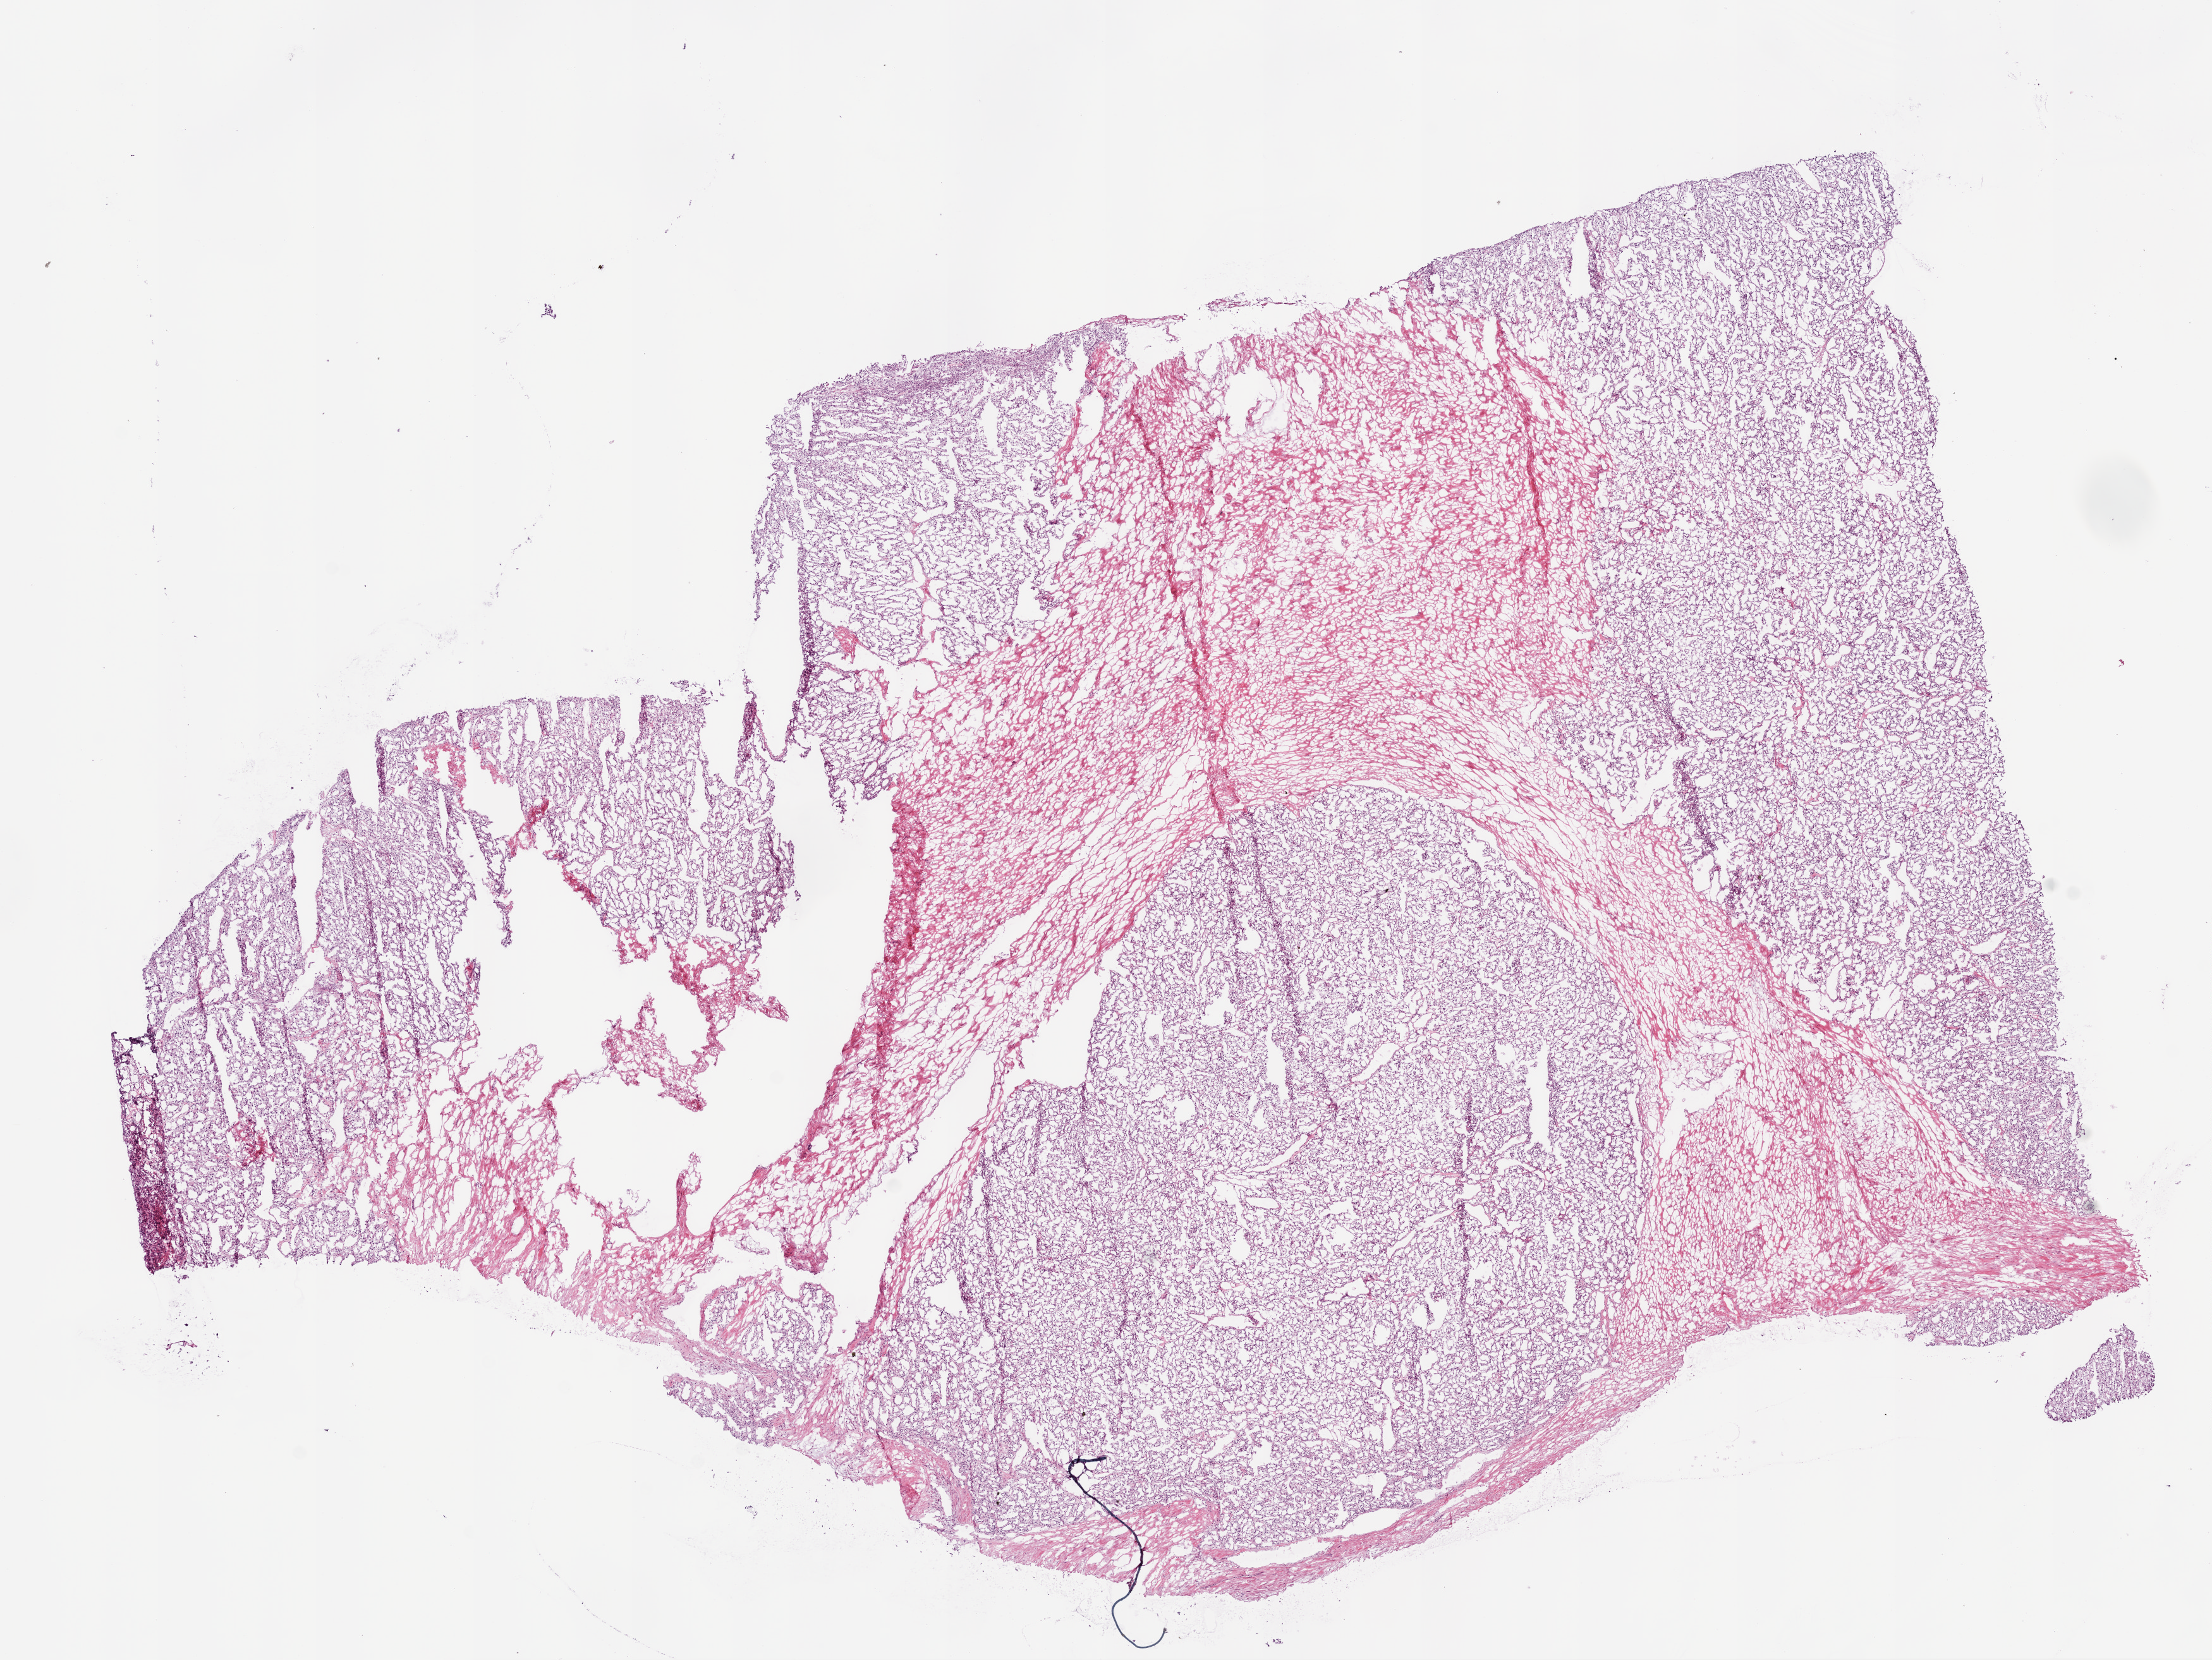
Digitized H&E-stained tissue section (whole slide), low-resolution overview of the scanned area, about 14.0 x 10.5 mm (slide scanned at 20x). Frozen section from the bottom of the tissue portion. Kidney, primary tumour sample. Patient: male, age at initial diagnosis 72 years. Histologic grade: G3 (poorly differentiated). Pathologist review of this section (percent, as recorded): tumour cells 70%, tumour nuclei 80%, normal cells 0%, stromal cells 30%, necrosis 0%.
TNM: T3a NX M0. Diagnosis: Clear cell adenocarcinoma, NOS. AJCC pathologic stage: III.